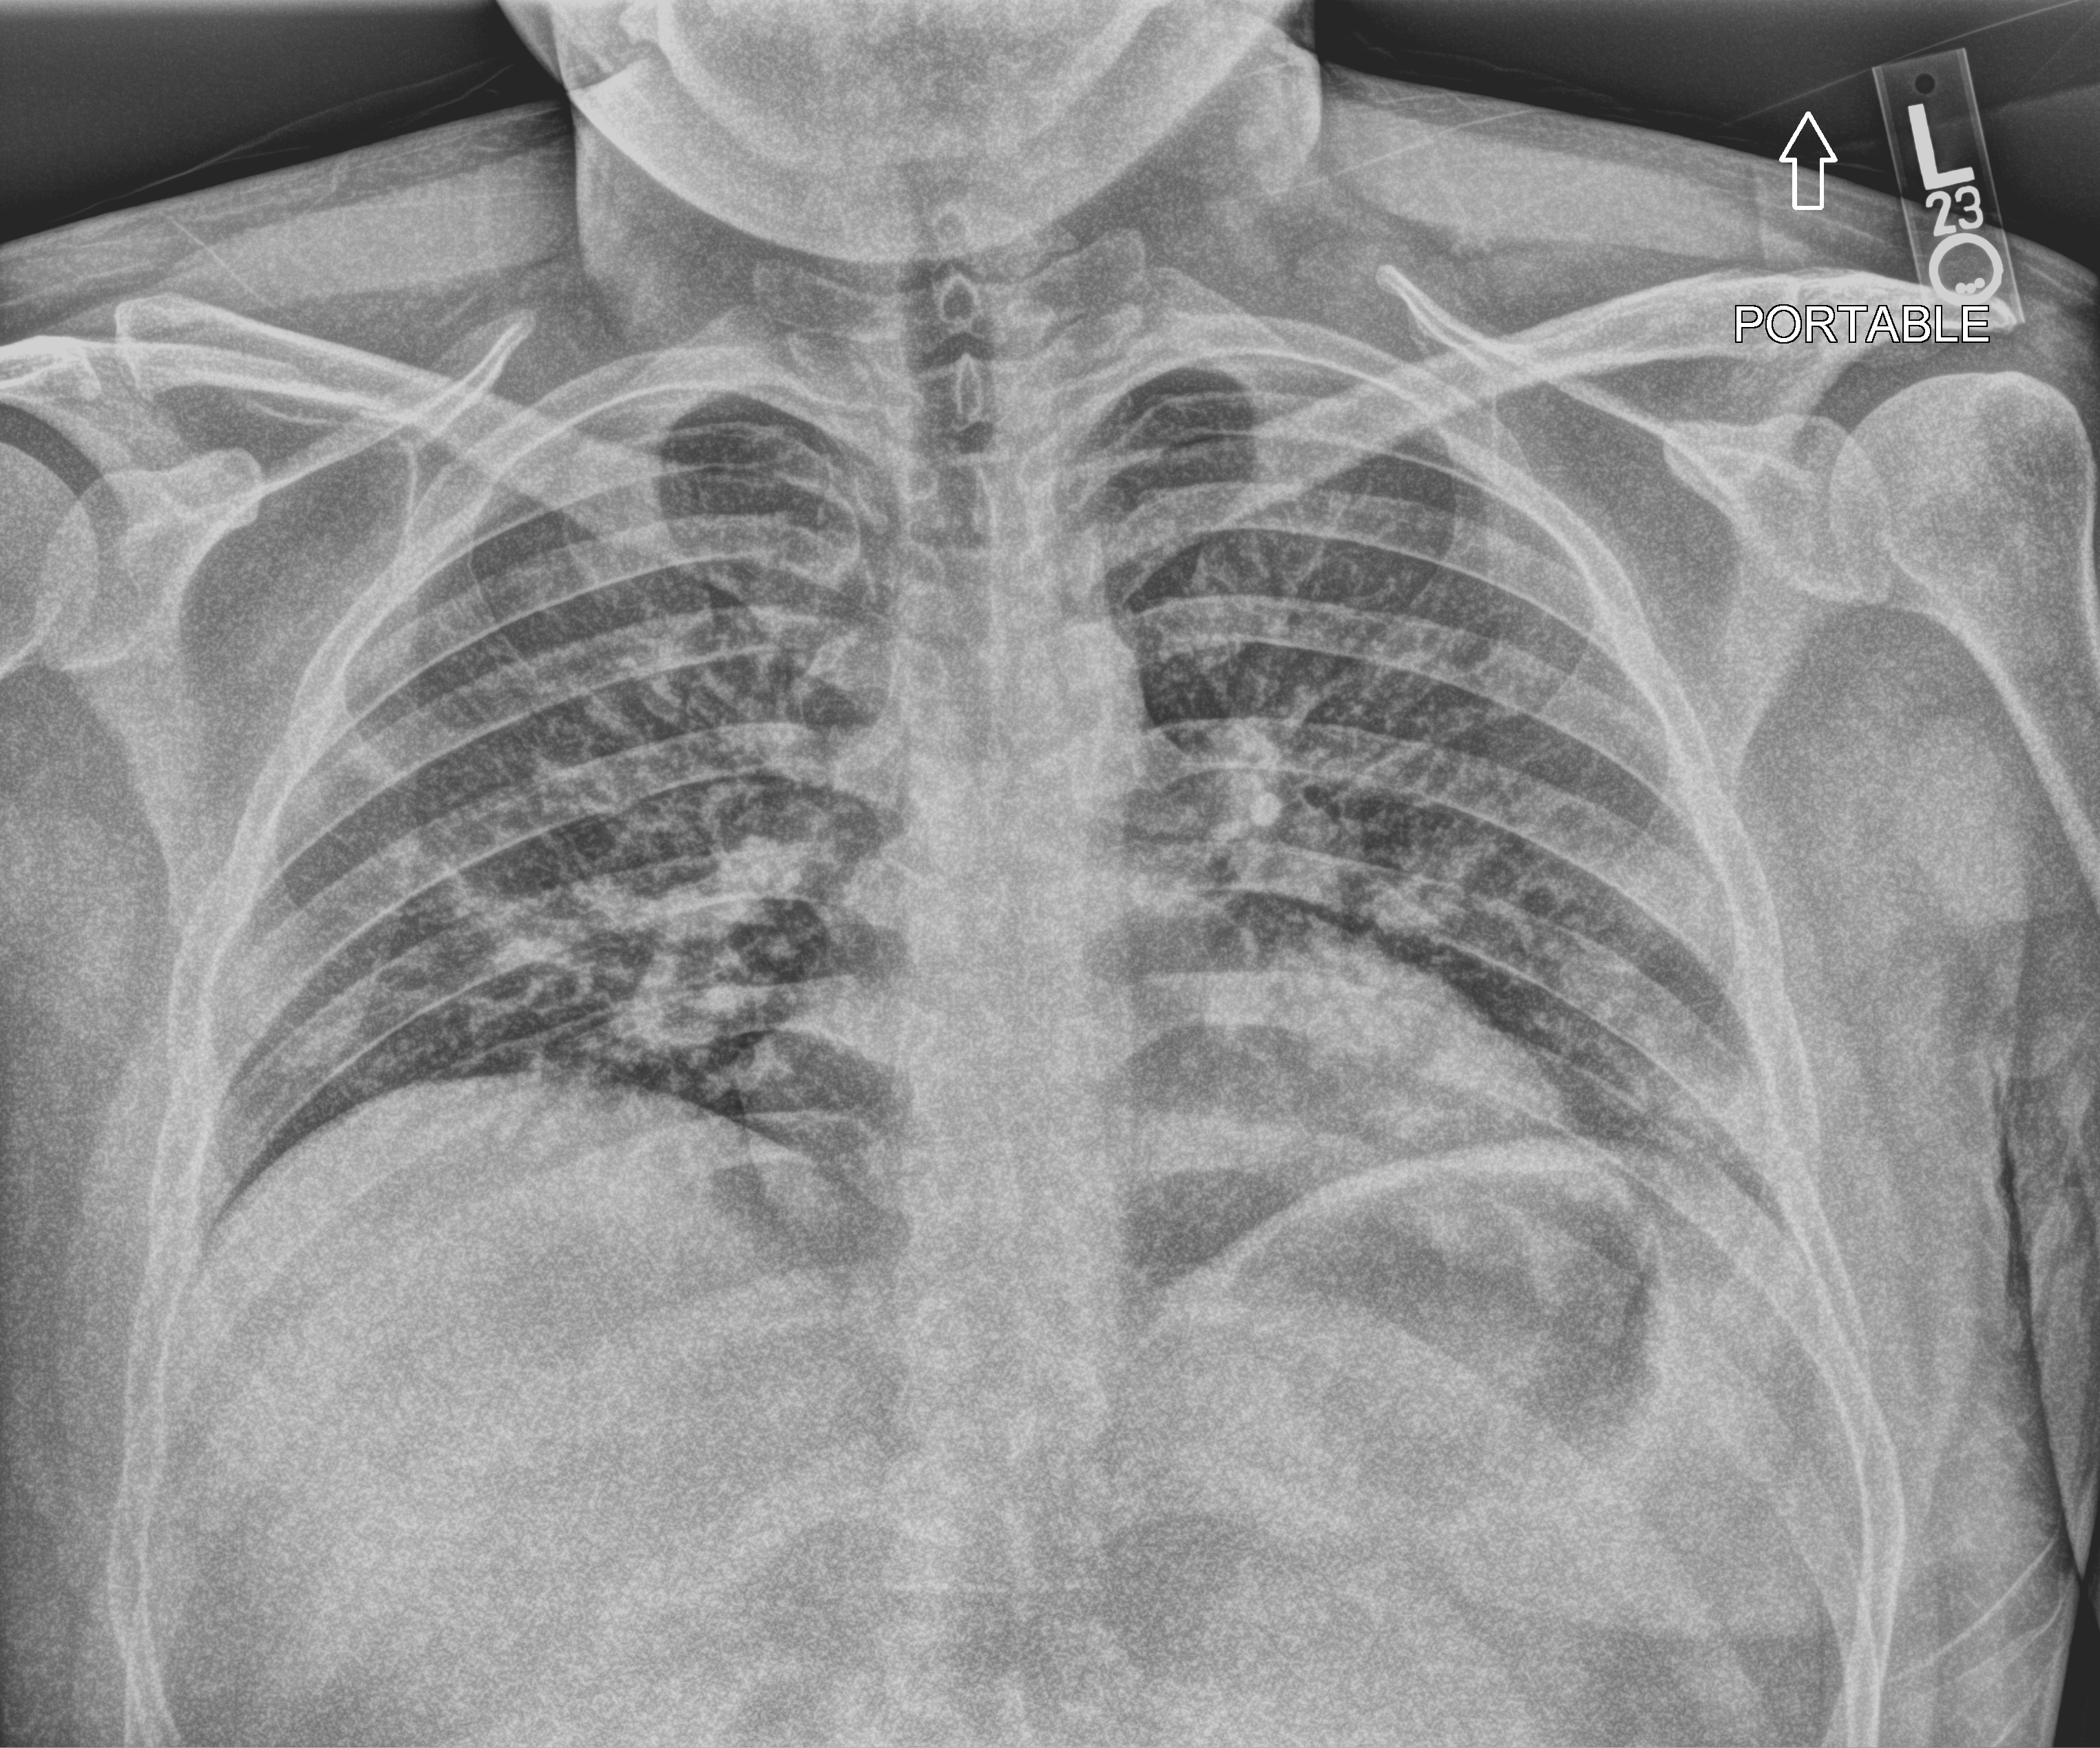
Chest X-ray (portable); anteroposterior (AP) projection. Patient hospitalised with COVID-19; male, aged 18–59 years.
Admission-level facts for this patient (not findings on this image; timing relative to this image not recorded): smoking status (admission record): never; admitted to intensive care during this hospital stay: no; diabetes (admission record): no.